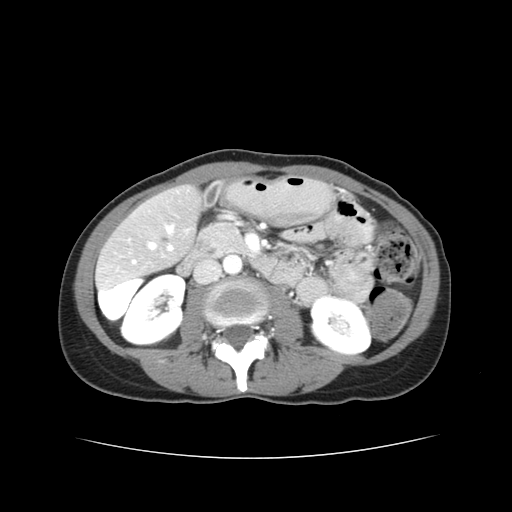
Contrast-enhanced abdominal CT, one axial slice. Slice 11 of 38 in the series (ordered by position). Reconstruction kernel STANDARD. 120 kVp. Soft-tissue window (W 400 / L 40 HU). 5 mm slice thickness. 512 × 512 image matrix, field of view 340 × 340 mm. Female patient, age 54 years. From the clinical record (not read from this slice): diagnosis: colorectal cancer liver metastases, imaged before liver resection; multiple liver metastases: yes; largest metastasis: 1.1 cm; chemotherapy before resection: yes.
Structures marked on this image (expert manual segmentation):
- hepatic veins: bounding box <150,227,173,249> (left, top, right, bottom; pixels)
- liver: <98,188,197,283>
- portal vein (with intrahepatic branches): <133,246,173,264>